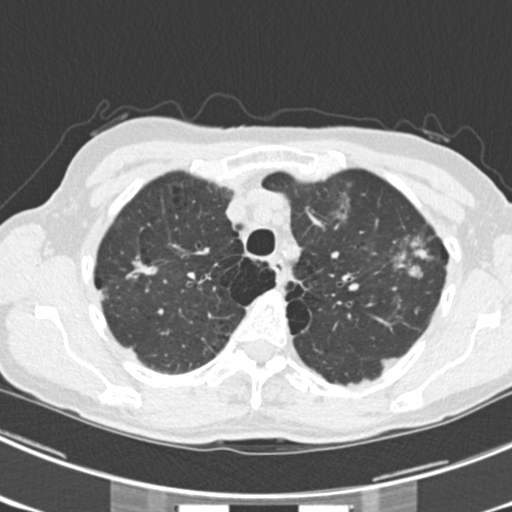
Axial slice from a low-dose chest CT screening exam; third annual screen; lung window (W 1500 / L -600 HU); 2 mm slice thickness; standard (soft-tissue) reconstruction kernel (B30f); 120 kVp; slice 51 of 225 in the series; 512 × 512 image matrix. Female, age 63 years at enrolment. Current smoker at enrolment.
Expert-annotated lung lesion, box from (x=378, y=221) to (x=451, y=281) px. The screening reader recorded 9 non-calcified nodules or masses ≥4 mm on this exam (left upper lobe, right upper lobe, left upper lobe, left lower lobe, right middle lobe, left lower lobe, left lower lobe, right lower lobe, right lower lobe); which of them this box marks is not recorded. Official screen result: positive, other. Lung cancer was diagnosed 15 days after this screen: bronchiolo-alveolar adenocarcinoma, NOS, right upper lobe, right middle lobe, right lower lobe, left upper lobe, left lower lobe, moderately differentiated (G2), stage IV (AJCC 6th edition).